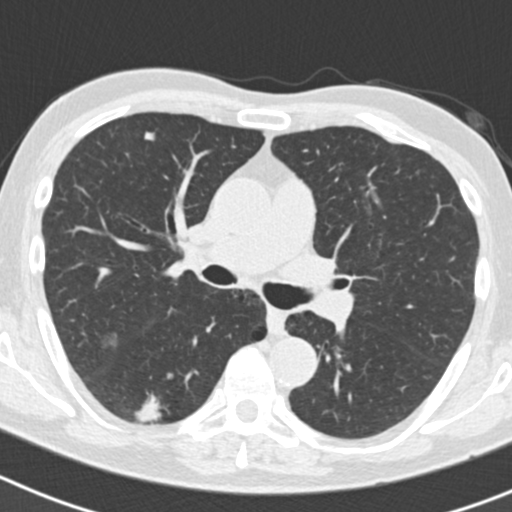
Chest CT (low-dose screening protocol), one axial image, second annual screen, lung window (W 1500 / L -600 HU), 2 mm slice thickness, 120 kVp, slice 71 of 186 in the series. Male, age 70 years at enrolment. Current smoker at enrolment.
Expert reader's lesion annotation, bounding box [x1, y1, x2, y2] px = [135, 380, 195, 434]. The screening reader recorded 5 non-calcified nodules or masses ≥4 mm on this exam; which of them this box marks is not recorded. Official screen result: positive, other. Later outcome: lung cancer diagnosed 622 days after this screen — bronchiolo-alveolar adenocarcinoma, NOS, right lower lobe, poorly differentiated (G3), stage IB (AJCC 6th edition), 30 mm at pathology.